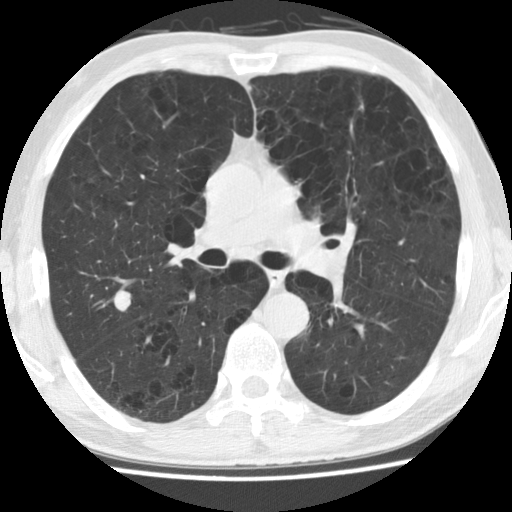
Axial slice from a low-dose chest CT screening exam, baseline annual screen, lung window (W 1500 / L -600 HU), standard (soft-tissue) reconstruction kernel (STANDARD), slice 69 of 158 in the series, 512 × 512 image matrix. Male, age 62 years at enrolment.
Lesion marked by an expert reader, box from (x=90, y=265) to (x=148, y=327) px. The screening reader recorded 2 non-calcified nodules or masses ≥4 mm on this exam (left upper lobe, right upper lobe); which of them this box marks is not recorded. Official screen result: positive, change unspecified: nodule(s) >= 4 mm or enlarging nodule(s), mass(es), or other non-specific abnormalities suspicious for lung cancer. Lung cancer was diagnosed 288 days after this screen: oat cell carcinoma, right upper lobe, undifferentiated (G4), stage IV (AJCC 6th edition), 30 mm at pathology.